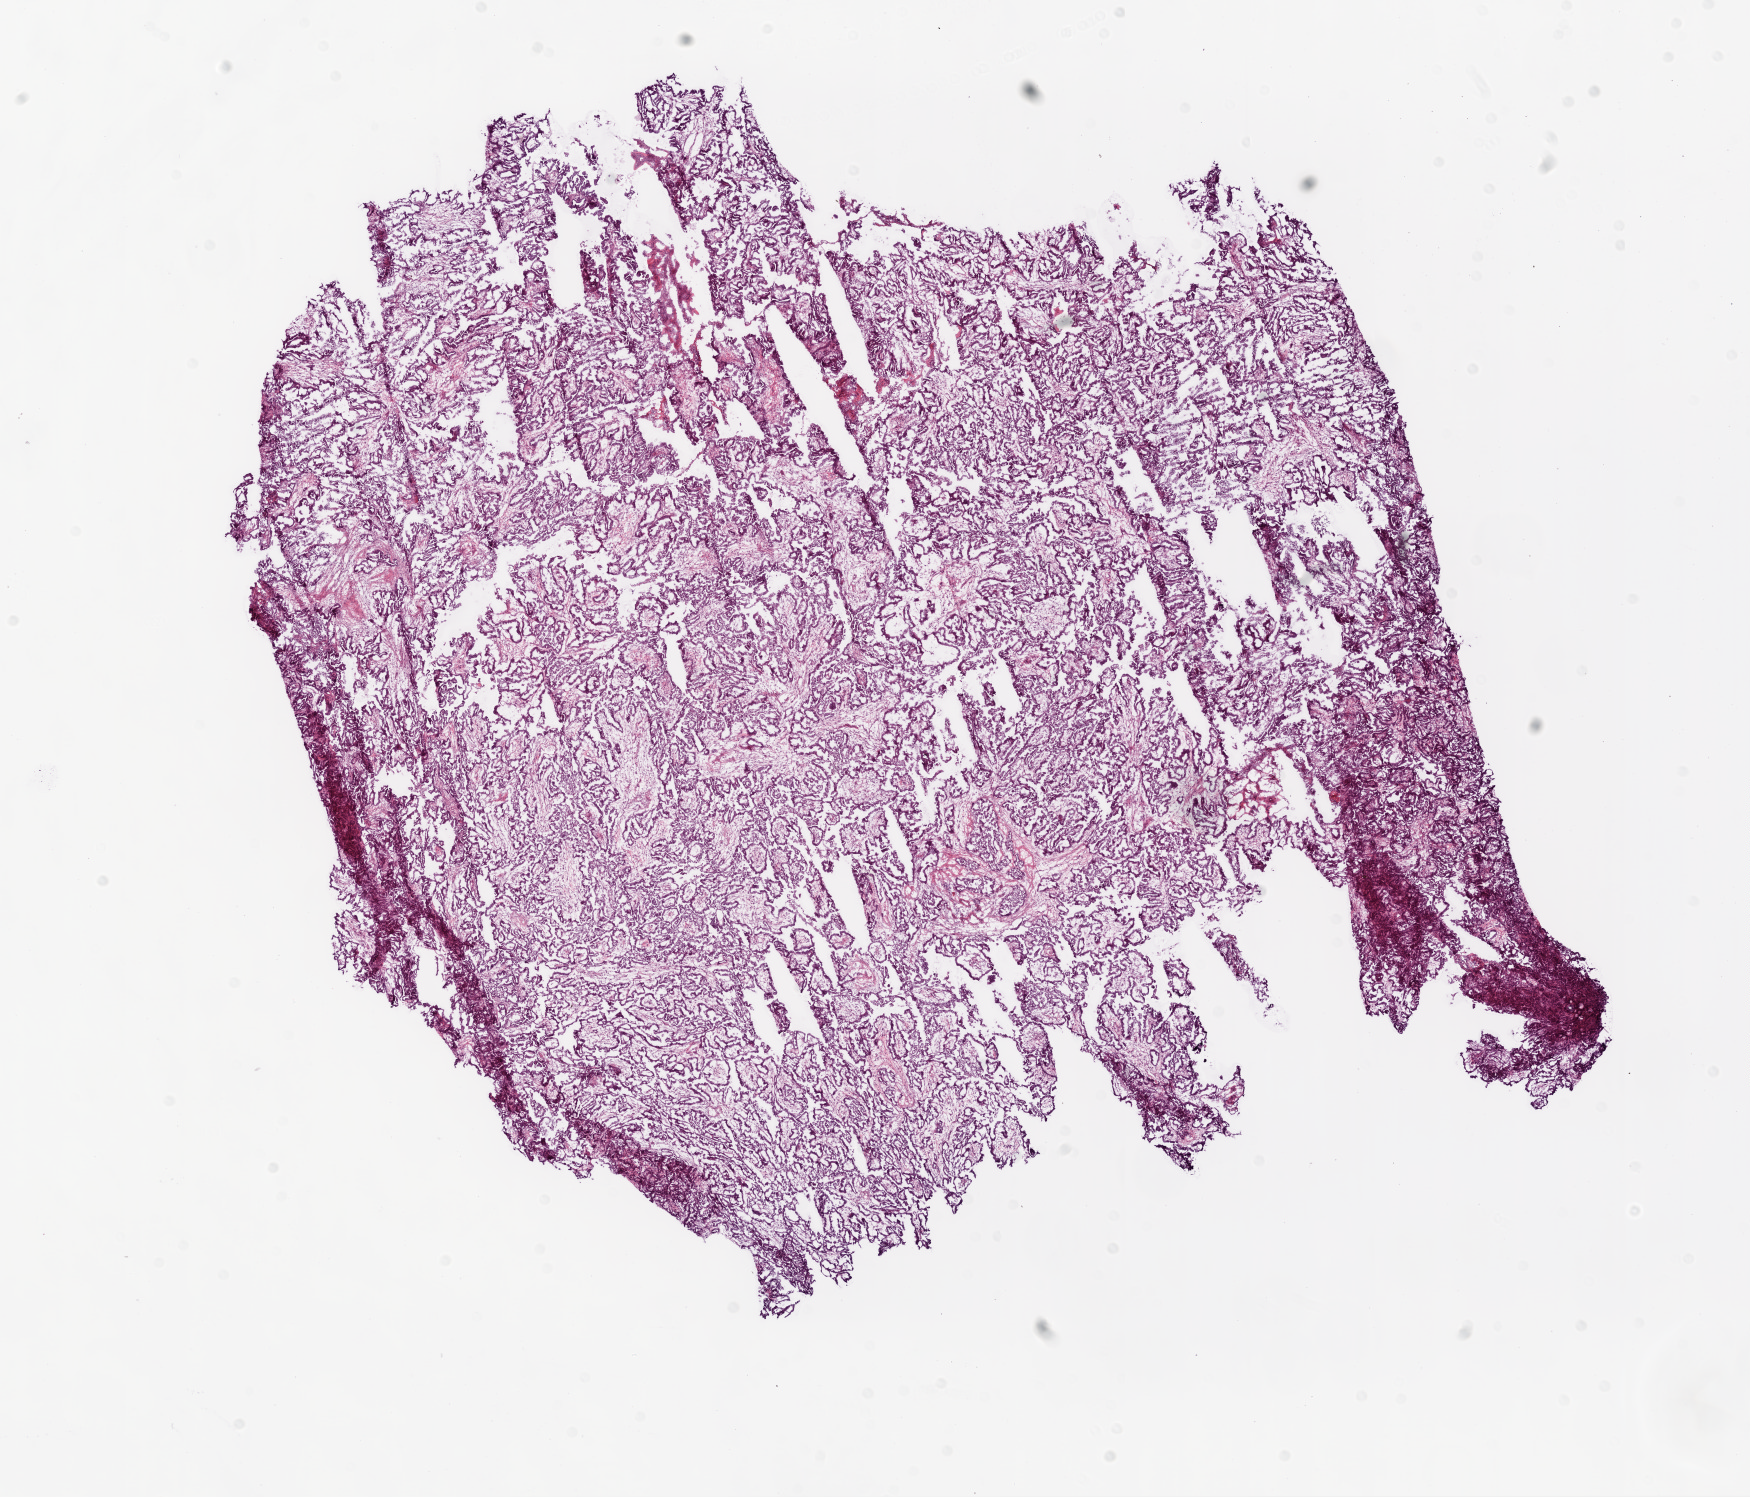
Whole-slide histology image, Hematoxylin and eosin (H&E) stained — a low-resolution overview of the entire scanned area, about 14.0 x 12.0 mm (slide scanned at 20x), frozen section, primary tumour sample from the ovary. Female, age 72 years at initial diagnosis. Slide review estimates, as recorded: tumour cells 95%, tumour nuclei 80%.
Histologic diagnosis: Serous cystadenocarcinoma, NOS.